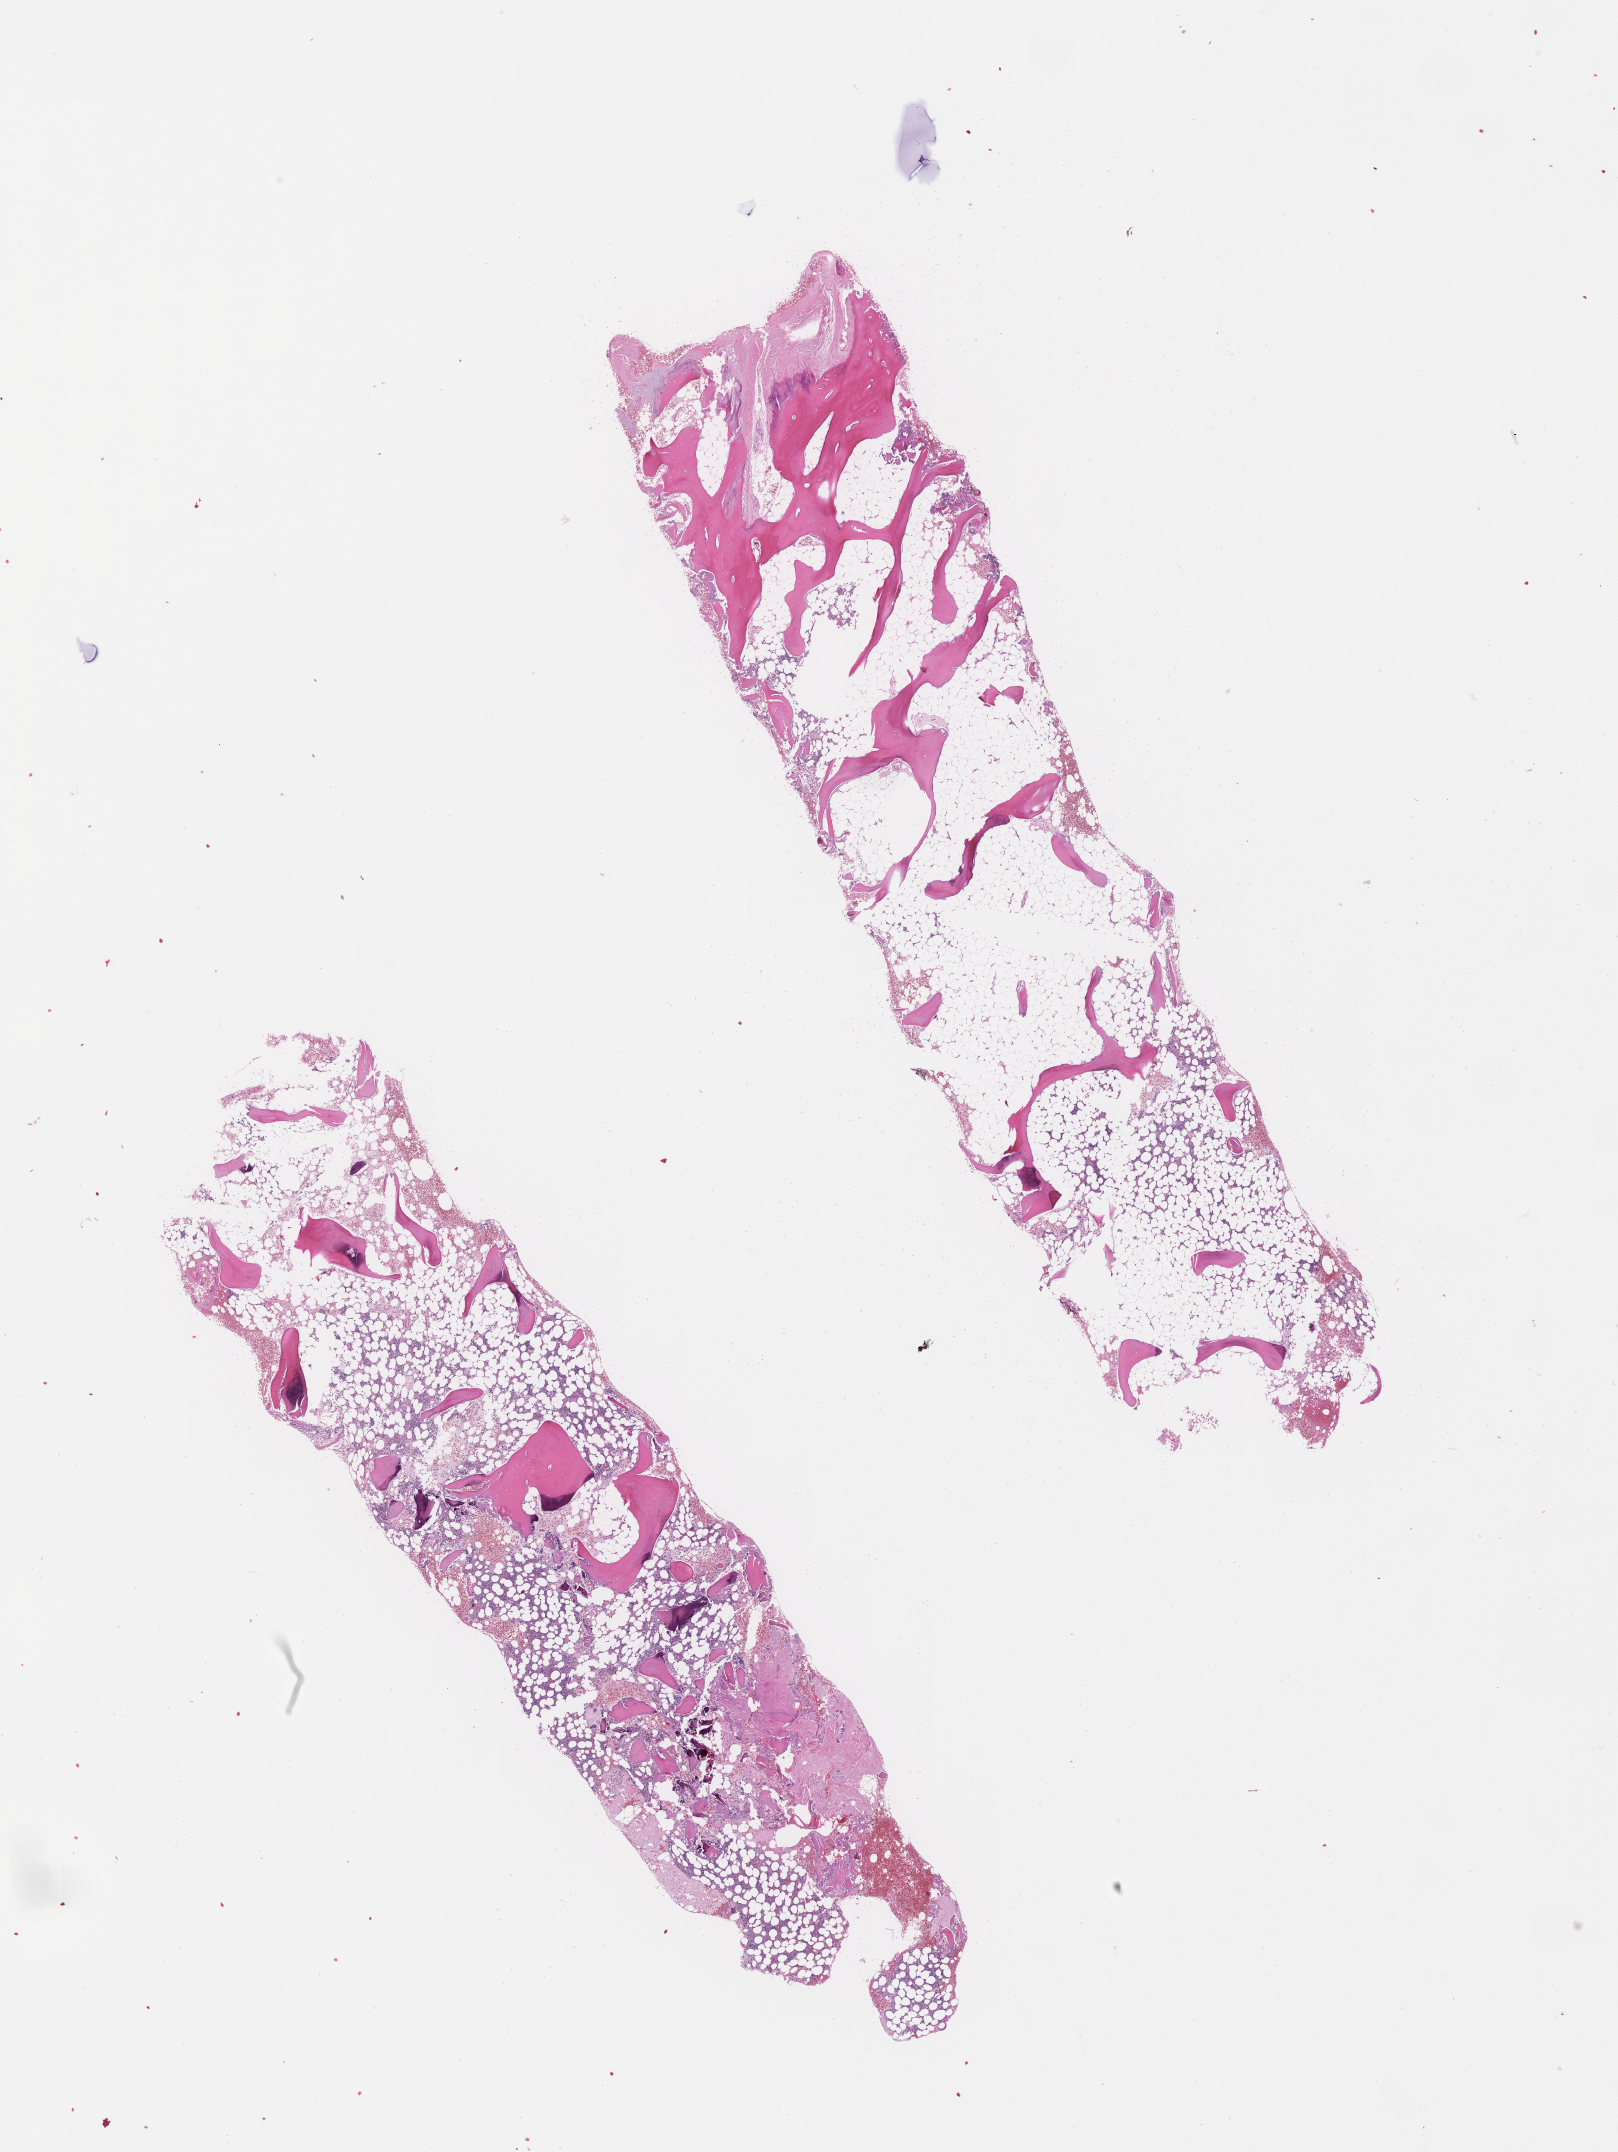
Whole-slide image, H&E stain — a low-resolution overview of the entire scanned area, about 13.1 x 17.4 mm. Formalin-fixed paraffin-embedded section. Tissue site: bone marrow. Archival tissue. Male patient.
* this section: primary tumour tissue
* diagnosis: Plasma Cell Myeloma